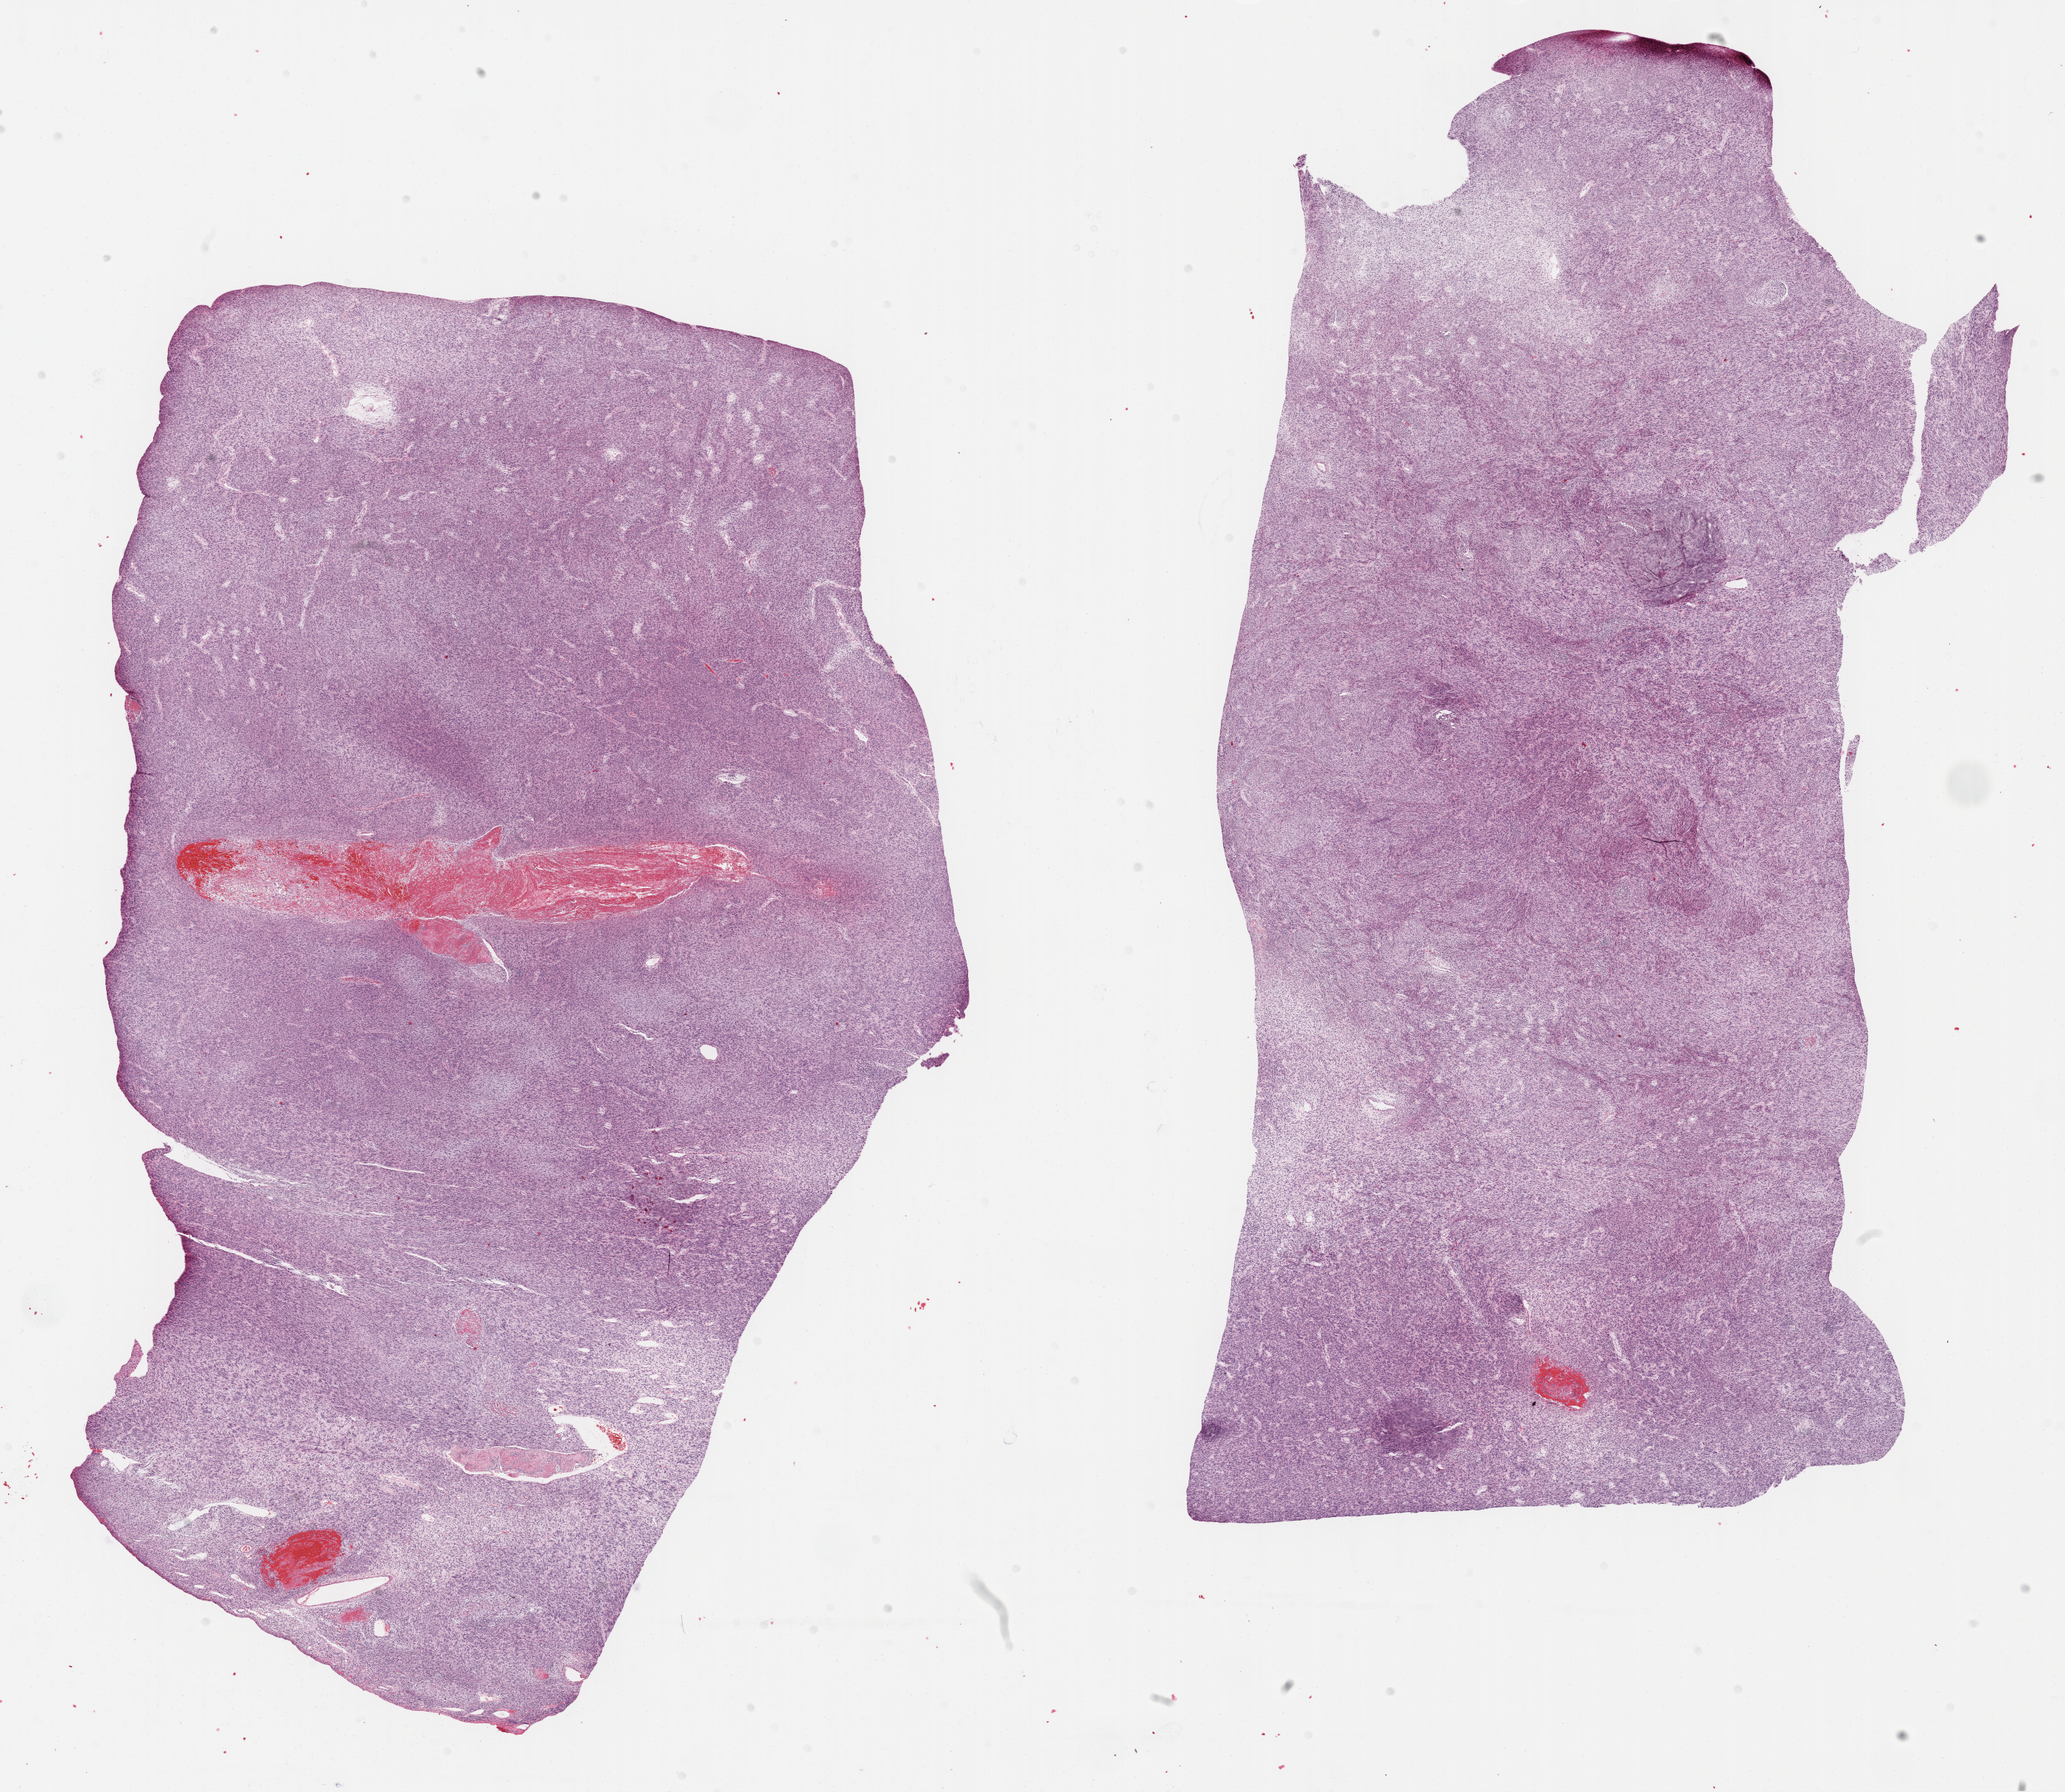
Digitized H&E-stained tissue section (whole slide), shown as a low-resolution overview of the whole scanned area (about 22.7 x 19.7 mm, from a 40x scan), formalin-fixed paraffin-embedded (FFPE) diagnostic section, retroperitoneum and peritoneum, primary tumour sample. Male, age 52 years at initial diagnosis.
Diagnosis: Undifferentiated sarcoma (retroperitoneum).